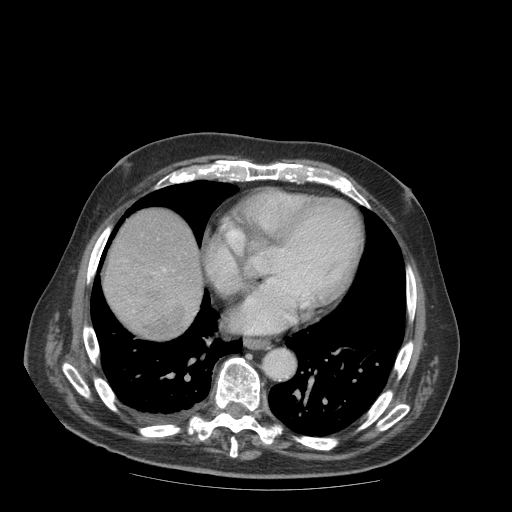
Contrast-enhanced abdominal CT (liver protocol), one axial slice. Position 89 of 99 along the scan axis. Reconstruction kernel STANDARD. Soft-tissue window (W 400 / L 40 HU). 512 × 512 image matrix. Case-level facts recorded for this patient, not image findings: diagnosis: hepatocellular carcinoma (patient treated with transarterial chemoembolisation; whether this scan precedes or follows treatment is not stated here); TNM stage (as recorded): Stage-IIIB; Child-Pugh class: A; tumour differentiation: well differentiated.
Structures marked on this image (semi-automatically segmented with operator editing):
- abdominal aorta: box from (x=263, y=350) to (x=295, y=379) px
- liver parenchyma outside the tumour (the mass and vessels are separate outlines, so this box may not span the whole liver): (x=102, y=208)–(x=202, y=338)
- mass: (x=104, y=262)–(x=196, y=339)
- liver vessels: (x=162, y=268)–(x=166, y=271)